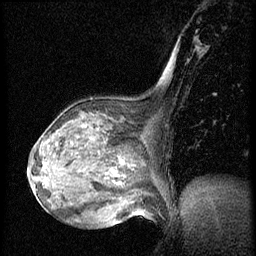
Breast MRI (dynamic contrast-enhanced), one sagittal slice. Dynamic contrast-enhanced series, image 2 of 3 at this slice position (ordered by acquisition). 1.5 T. TE 4.2 ms, TR 20.4 ms. 2 mm slice thickness. 256 × 256 image matrix, field of view 200 × 200 mm. Female patient, age 64 years. Case-level facts recorded for this patient, not image findings: setting: breast cancer imaged before/during neoadjuvant chemotherapy; receptor status: HR-positive, HER2-negative.
Structures marked on this image (semi-automatically segmented with operator editing):
- analysis volume of interest (the breast-tissue region the enhancement analysis was run in; not a lesion): bounding box <48,102,142,186> (left, top, right, bottom; pixels)
- tumour enhancement mask (voxels above the 70 % enhancement threshold inside the analysis volume of interest): <110,159,124,176>